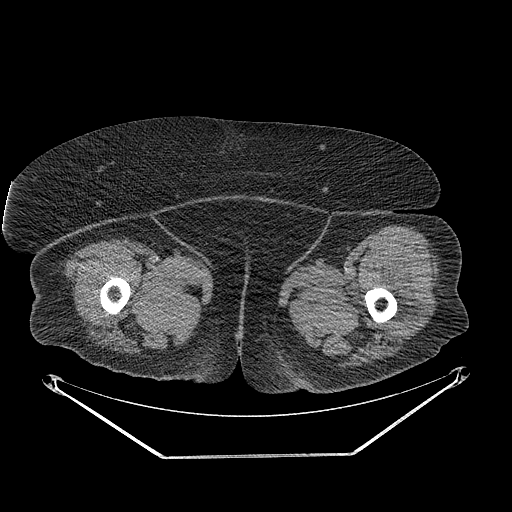
CT of an extremity soft-tissue mass (from a PET/CT study), one axial slice; slice 256 of 267 in the series (ordered by position); 140 kVp; soft-tissue window (W 400 / L 40 HU); 512 × 512 image matrix, field of view 500 × 500 mm. Female patient. From the clinical record (not read from this slice): histological type: undifferentiated – high grade; grade: high; site of the primary tumour: left thigh.
Structures marked on this image (expert contour drawn on MRI and transferred to this co-registered scan by the dataset authors):
- gross tumour volume including surrounding oedema: bounding box (x1, y1, x2, y2) in pixels: (383, 279, 421, 336)
- gross tumour volume (mass): (393, 308, 414, 323)